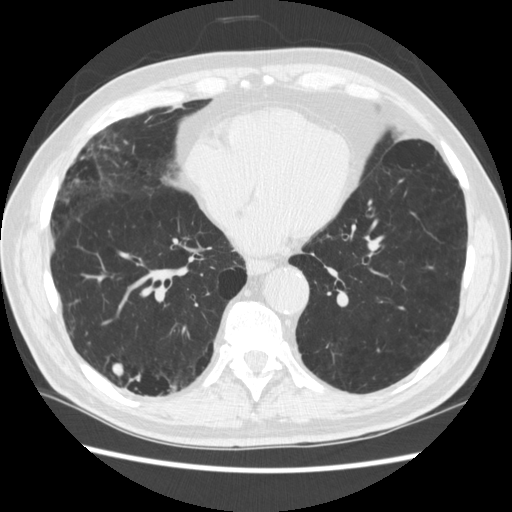
Low-dose screening chest CT, axial slice, third annual screen, lung window (W 1500 / L -600 HU), 1.25 mm slice thickness, standard (soft-tissue) reconstruction kernel (STANDARD), 120 kVp. Male participant, aged 70 years at enrolment. Former smoker at enrolment.
- Expert-annotated lung lesion, bounding box (x1, y1, x2, y2) in pixels: (131, 359, 177, 413).
- The screening reader recorded 4 non-calcified nodules or masses ≥4 mm on this exam (right lower lobe, right lower lobe, left lower lobe, left lower lobe); which of them this box marks is not recorded.
- Official screen result: positive, other.
- Participant outcome: lung cancer diagnosed 253 days after this screen — squamous cell carcinoma, NOS, right upper lobe, poorly differentiated (G3), stage IV (AJCC 6th edition).